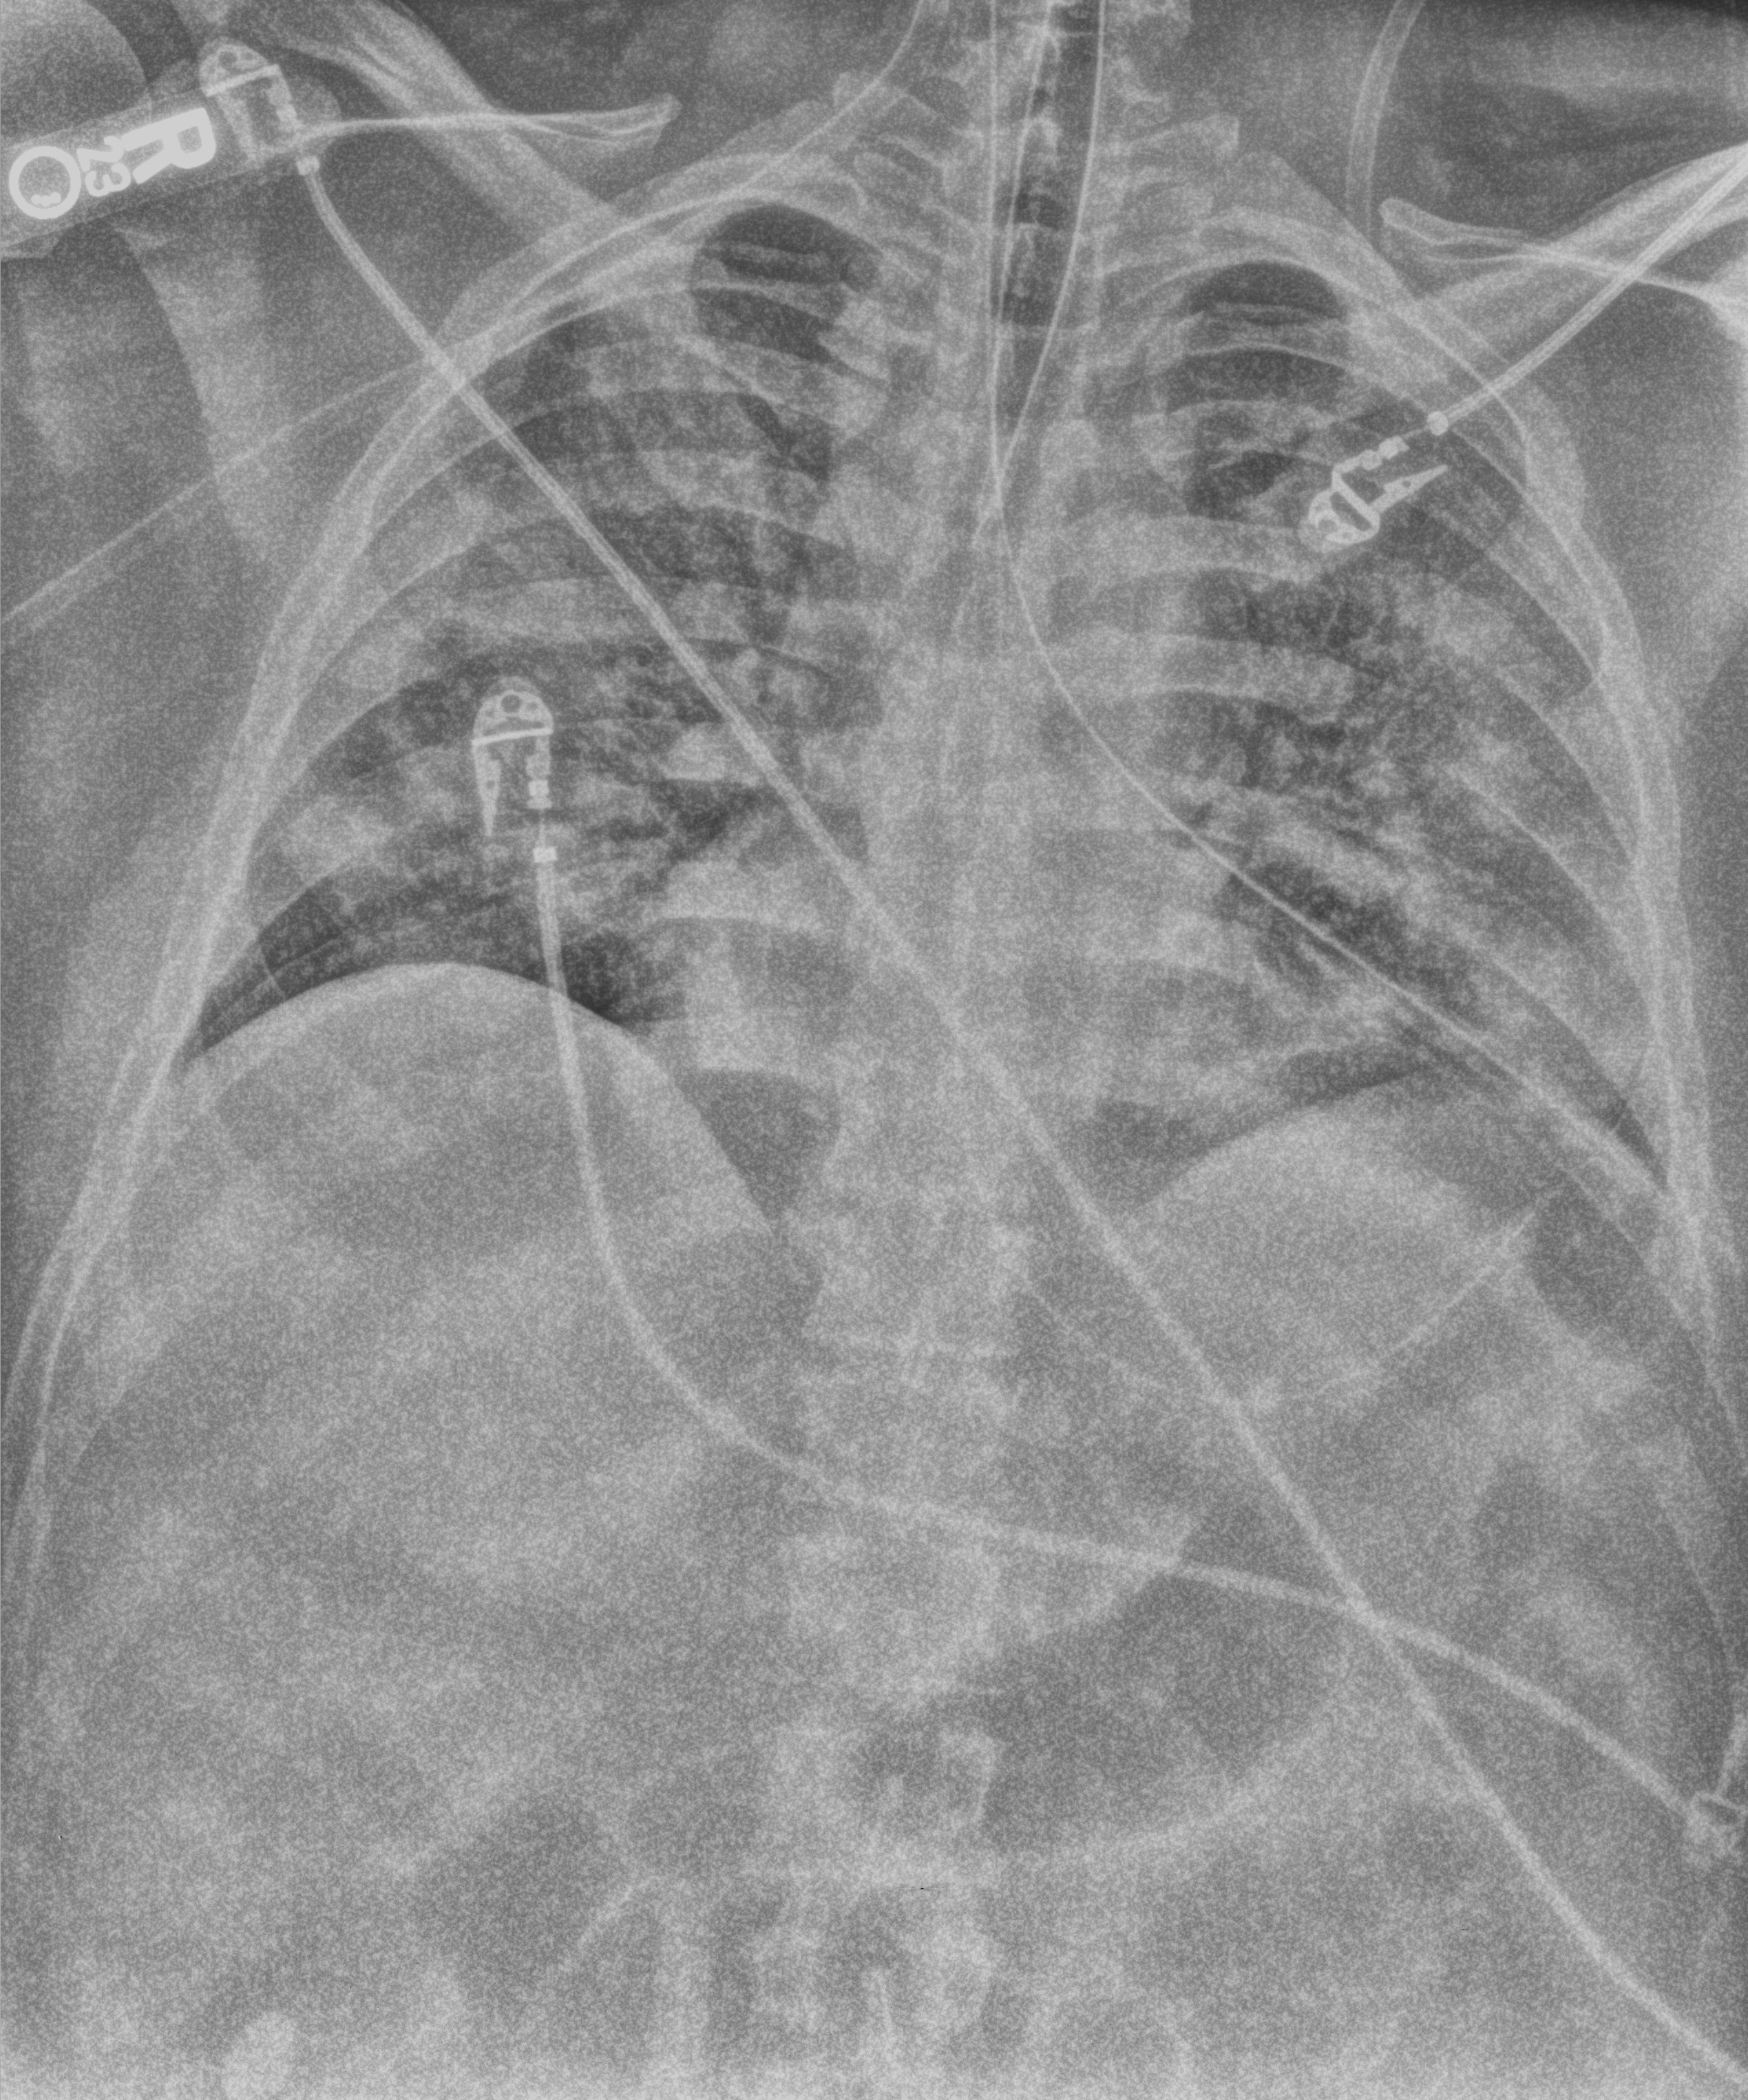
Chest X-ray (portable), anteroposterior (AP) projection. Adult patient hospitalised with COVID-19, age 18–59 years.
Hospital-stay facts (about this admission, not read from this image; timing relative to this image not recorded):
- other chronic lung disease (admission record): no
- COPD (admission record): no
- mechanically ventilated during this hospital stay: yes